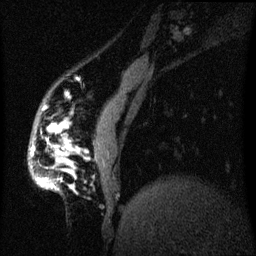
Breast MRI (dynamic contrast-enhanced), one sagittal slice; dynamic contrast-enhanced series, image 2 of 3 at this slice position (ordered by acquisition); 1.5 T; TE 4.2 ms, TR 8 ms; 256 × 256 image matrix, field of view 200 × 200 mm. Female patient, age 50 years.
Outlined on this slice (semi-automatically segmented with operator editing):
- analysis volume of interest (the breast-tissue region the enhancement analysis was run in; not a lesion): bounding box (x1, y1, x2, y2) in pixels: (34, 130, 57, 191)
- tumour enhancement mask (voxels above the 70 % enhancement threshold inside the analysis volume of interest): (40, 180, 44, 185)